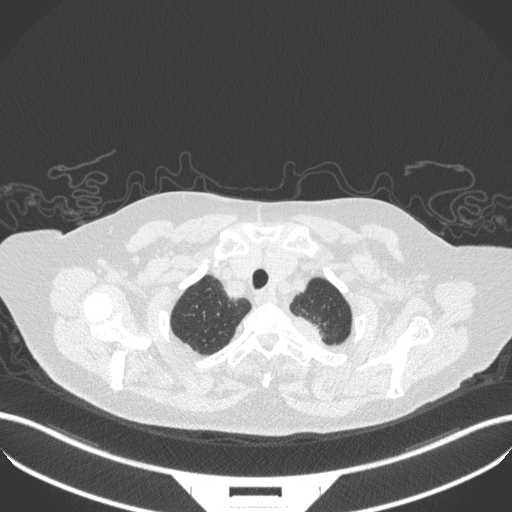
Chest CT, one axial slice; position 312 of 353 along the scan axis; 100 kVp; lung window (W 1500 / L -600 HU); 1 mm slice thickness; 512 × 512 image matrix, field of view 400 × 400 mm. Patient: female, 81 years. Case-level facts recorded for this patient, not image findings: clinical TNM (as recorded): T2a N0 M0.
Outlined on this slice (bounding box drawn by a radiologist):
- lung tumour (recorded histology: adenocarcinoma): bounding box [x1, y1, x2, y2] px = [291, 312, 331, 353]